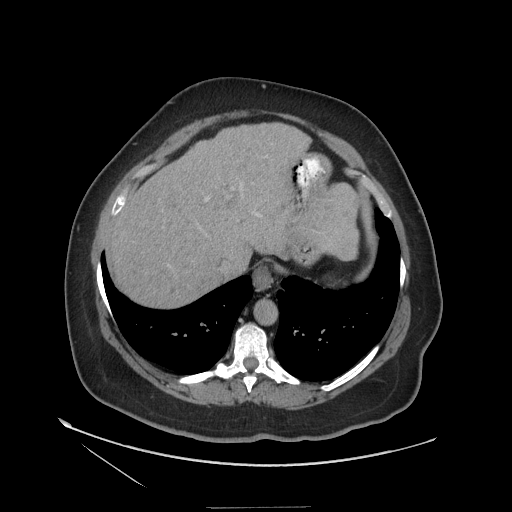
Contrast-enhanced abdominal CT (liver protocol), one axial slice; slice 95 of 127 in the series (ordered by position); 140 kVp; soft-tissue window (W 400 / L 40 HU); 2.5 mm slice thickness; 512 × 512 image matrix, field of view 480 × 480 mm. From the clinical record (not read from this slice): diagnosis: hepatocellular carcinoma (patient treated with transarterial chemoembolisation; whether this scan precedes or follows treatment is not stated here); TNM stage (as recorded): Stage-II; Child-Pugh class: A; tumour nodularity: multinodular; tumour size: 3 cm.
Structures marked on this image (semi-automatically segmented with operator editing):
- abdominal aorta: box from (x=254, y=299) to (x=276, y=325) px
- liver parenchyma outside the tumour (the mass and vessels are separate outlines, so this box may not span the whole liver): (x=106, y=124)–(x=358, y=306)
- liver vessels: (x=115, y=198)–(x=209, y=214)